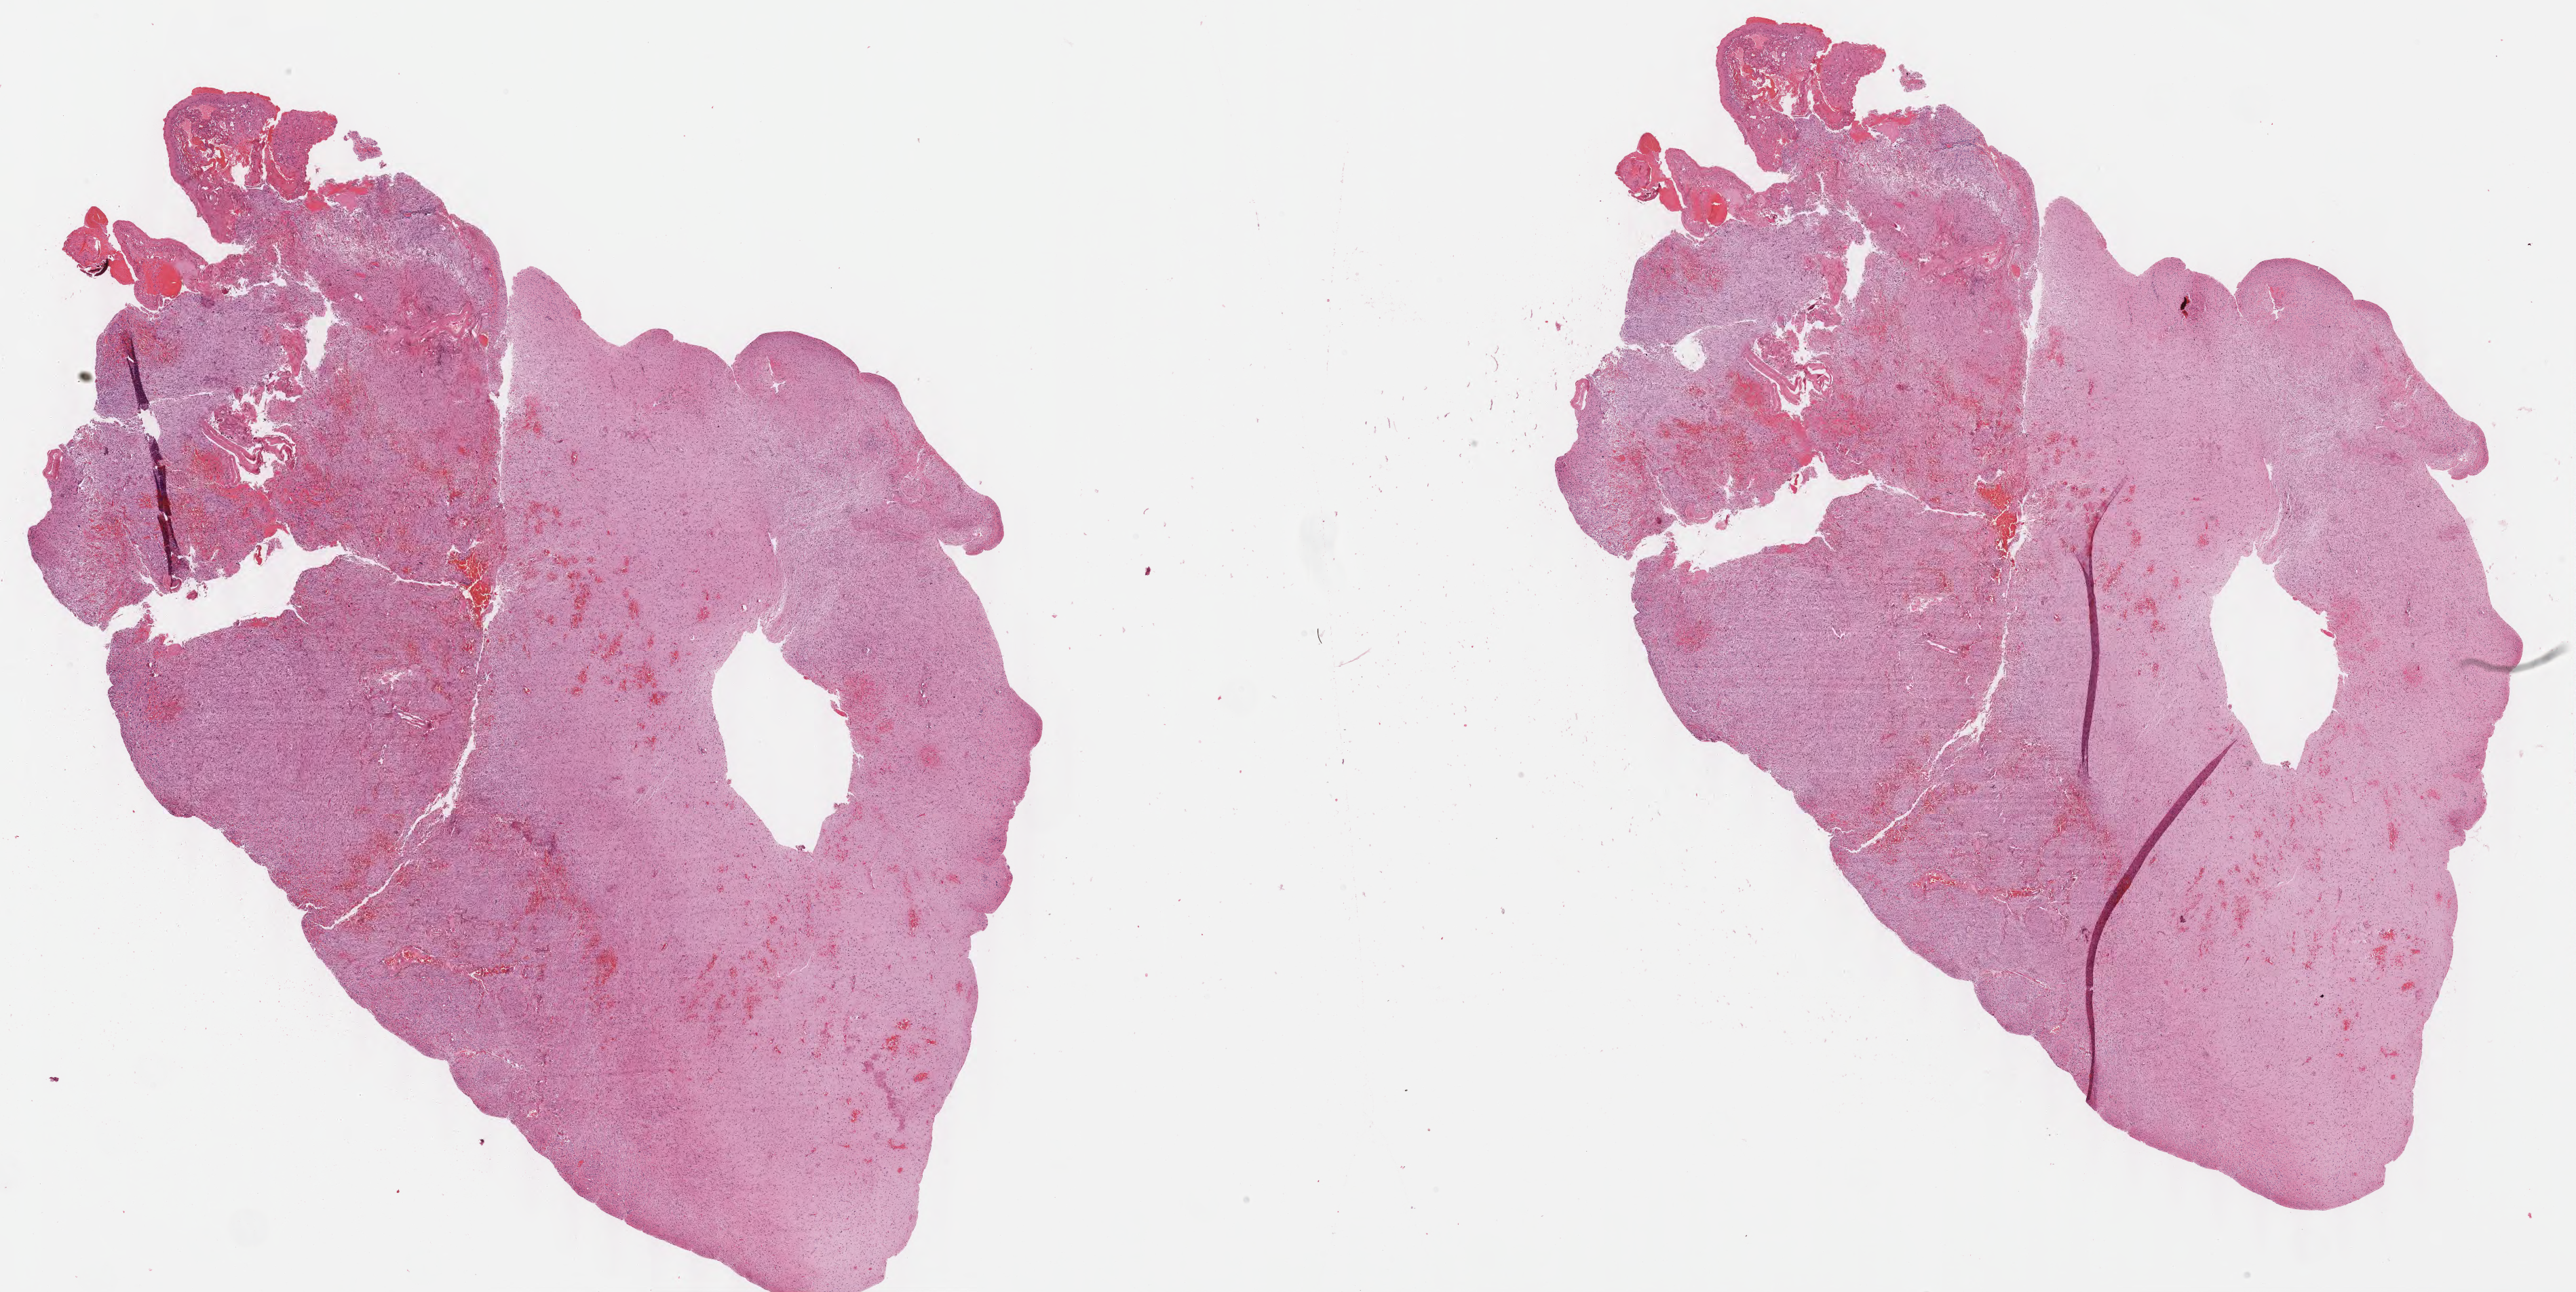
Digitized H&E-stained tissue section (whole slide), shown as a low-resolution overview of the whole scanned area (about 30.0 x 15.1 mm), formalin-fixed paraffin-embedded (FFPE) diagnostic section, brain, primary tumour sample. Female patient; age at initial diagnosis 25 years. Histologic grade: G2 (moderately differentiated).
Histologic diagnosis: Astrocytoma, NOS (cerebrum). Laterality: right.